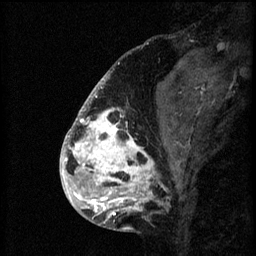
Breast MRI (dynamic contrast-enhanced), one sagittal slice. Slice 22 of 60 in the series (ordered by position). 3 images stored at this slice position (order not interpretable as contrast timing). 1.5 T. TE 4.2 ms, TR 8.2 ms. 2 mm slice thickness. 256 × 256 image matrix. Female patient, age 41 years.
Annotated regions visible in this slice (semi-automatic segmentation, software-assisted and operator-edited):
- analysis volume of interest (the breast-tissue region the enhancement analysis was run in; not a lesion): bounding box [x1, y1, x2, y2] px = [72, 108, 176, 205]
- tumour enhancement mask (voxels above the 70 % enhancement threshold inside the analysis volume of interest): [72, 108, 164, 205]